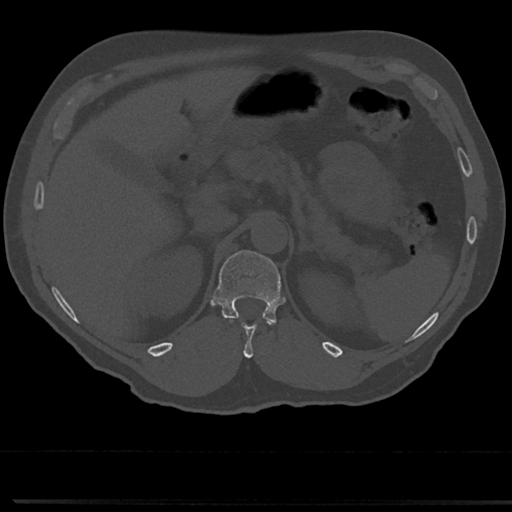
CT including the spine, one axial slice. 120 kVp. Bone window (W 1800 / L 400 HU). 512 × 512 image matrix, field of view 355 × 355 mm. Patient: male, 61 years. From the clinical record (not read from this slice): primary cancer: prostate.
Annotated regions visible in this slice (semi-automatic segmentation, software-assisted and operator-edited):
- T11 vertebra: box from (x=231, y=324) to (x=276, y=357) px
- T12 vertebra: (x=214, y=249)–(x=285, y=337)